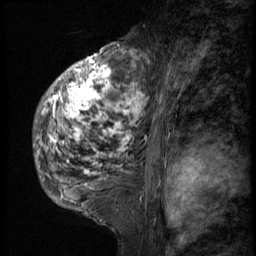
Breast MRI (dynamic contrast-enhanced), one sagittal slice. Position 36 of 58 along the scan axis. 3 images stored at this slice position (order not interpretable as contrast timing). 1.5 T. TE 4.2 ms, TR 9 ms. 2.5 mm slice thickness. 256 × 256 image matrix, field of view 180 × 180 mm. Patient: female, 50 years. From the clinical record (not read from this slice): setting: breast cancer imaged before/during neoadjuvant chemotherapy; receptor status: triple-negative.
Outlined on this slice (semi-automatic segmentation, software-assisted and operator-edited):
- analysis volume of interest (the breast-tissue region the enhancement analysis was run in; not a lesion): bounding box <33,48,139,214> (left, top, right, bottom; pixels)
- tumour enhancement mask (voxels above the 140 % enhancement threshold inside the analysis volume of interest): <34,50,139,202>